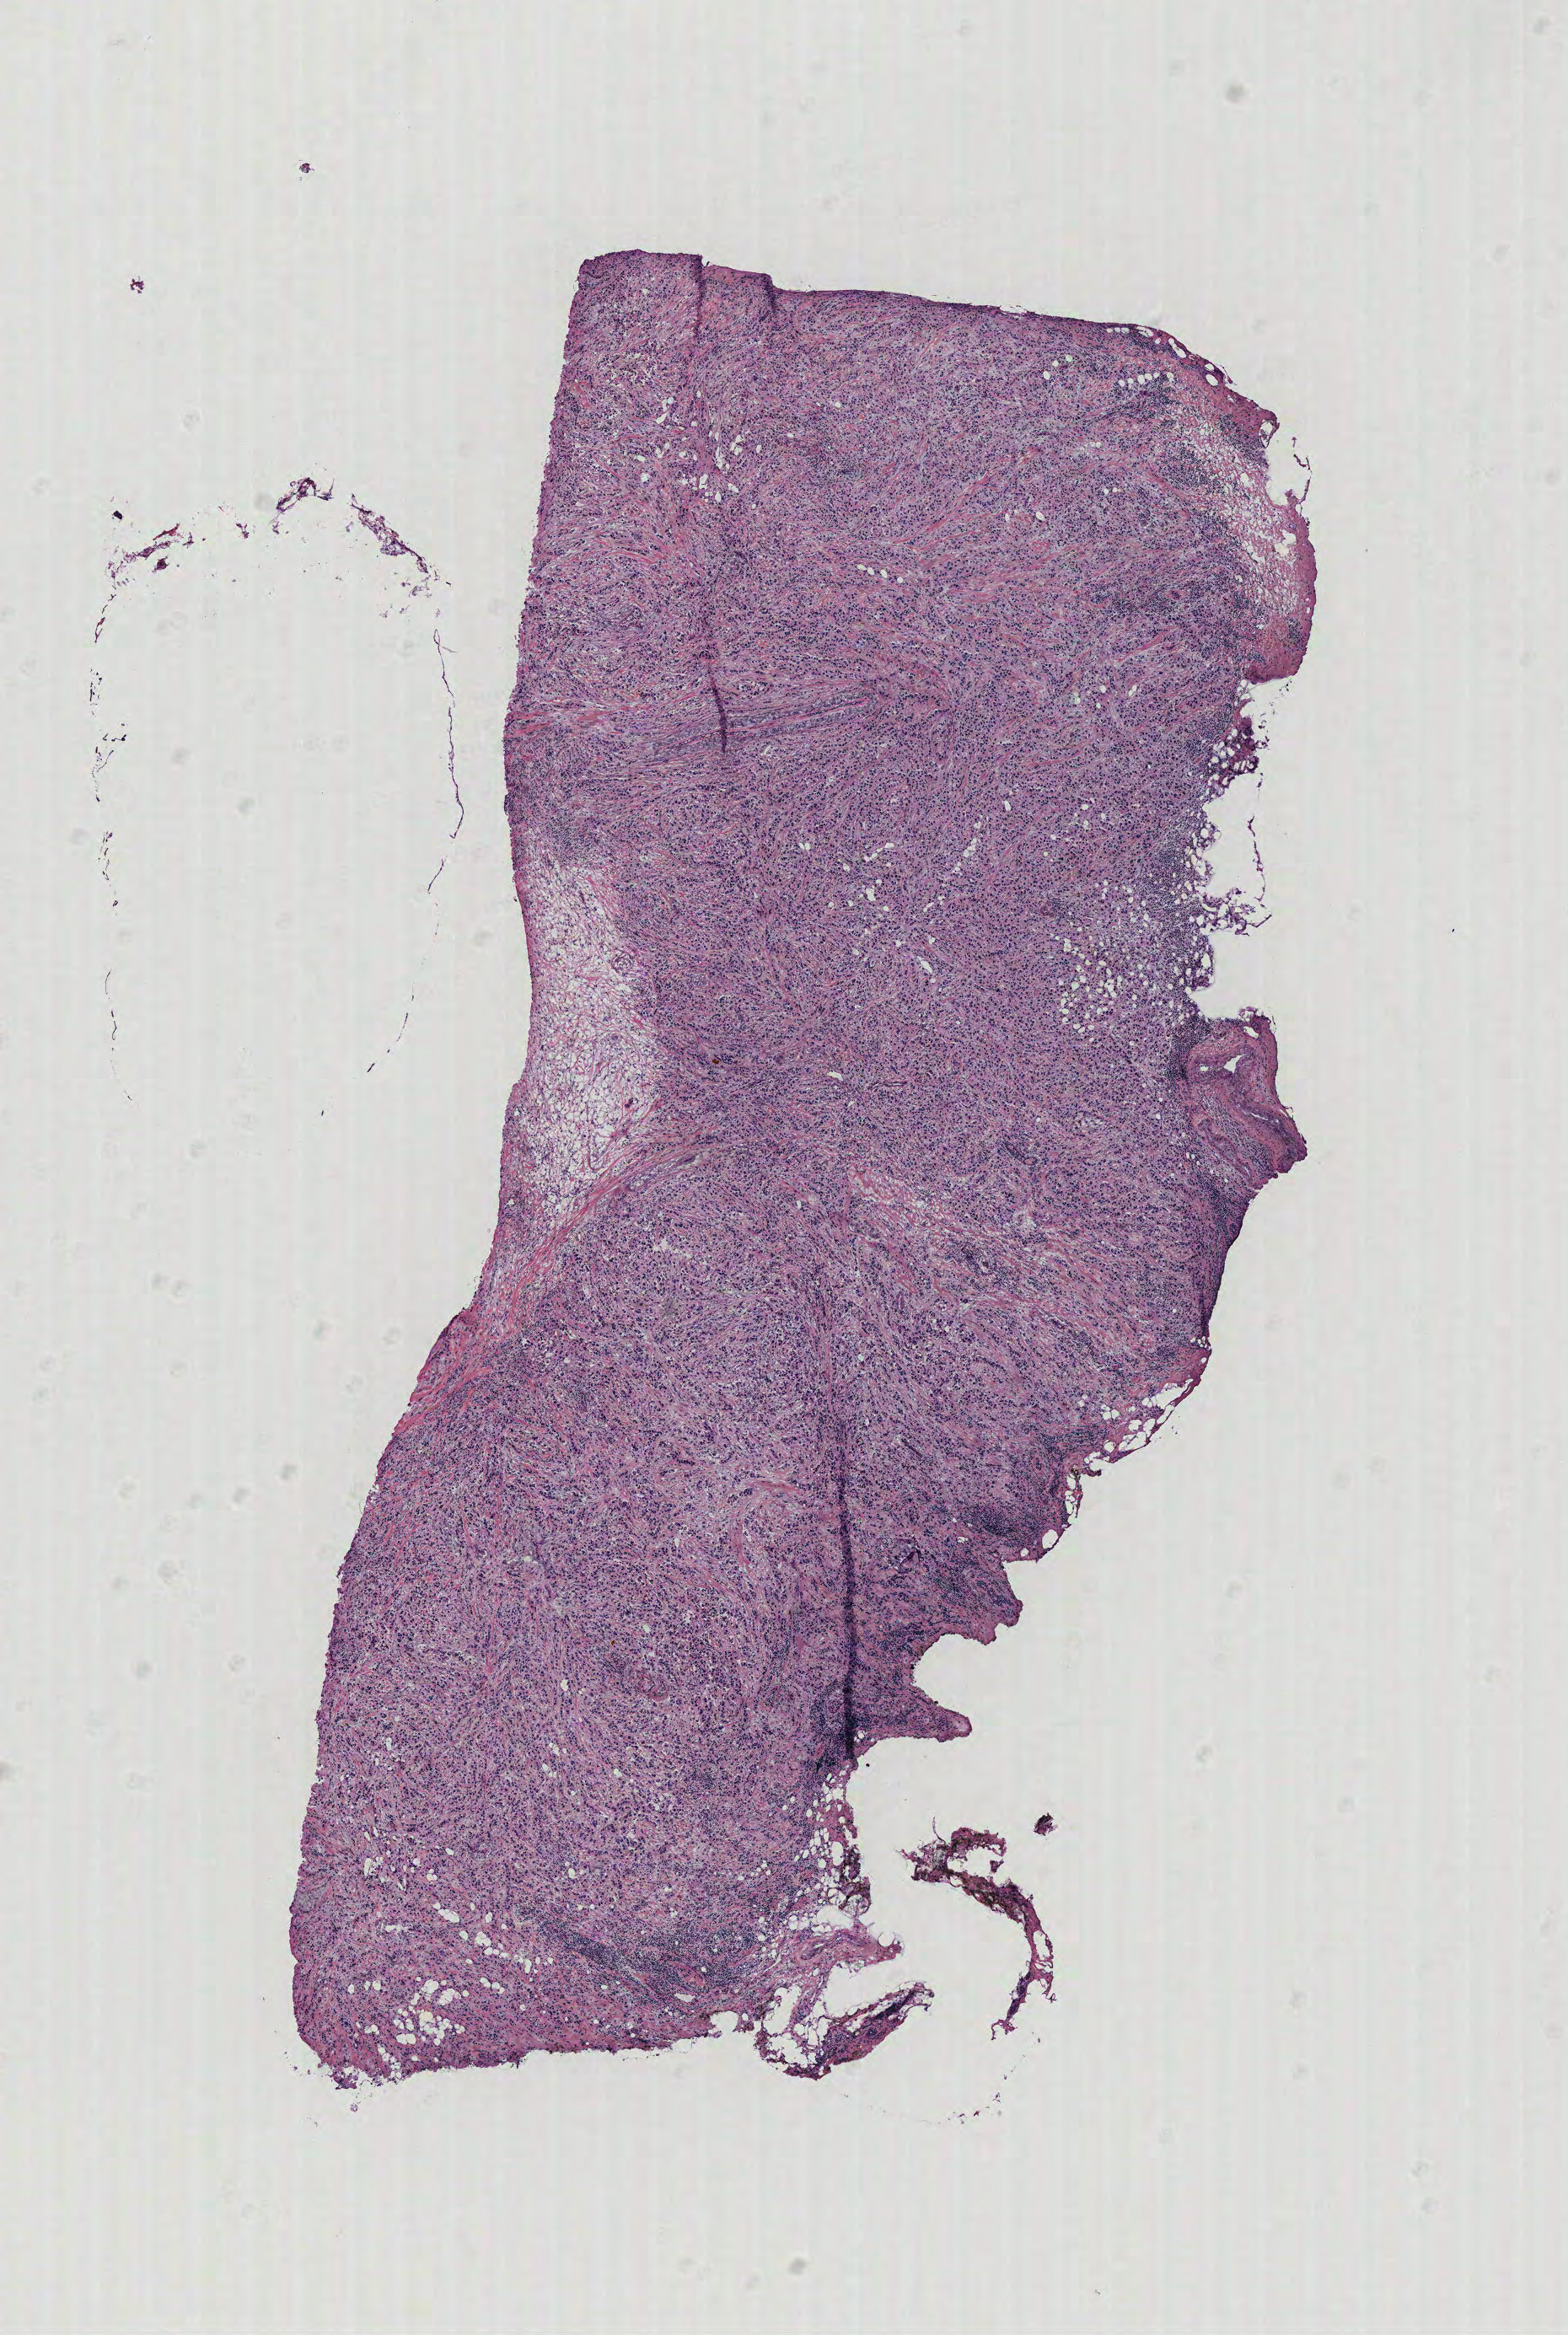
Hematoxylin and eosin (H&E) stained whole-slide image, shown as a low-resolution overview of the whole scanned area (about 7.4 x 11.1 mm, slide scanned at 40x). Breast, tissue type not recorded.
Patient diagnosis (cohort enrolment): breast cancer (breast).